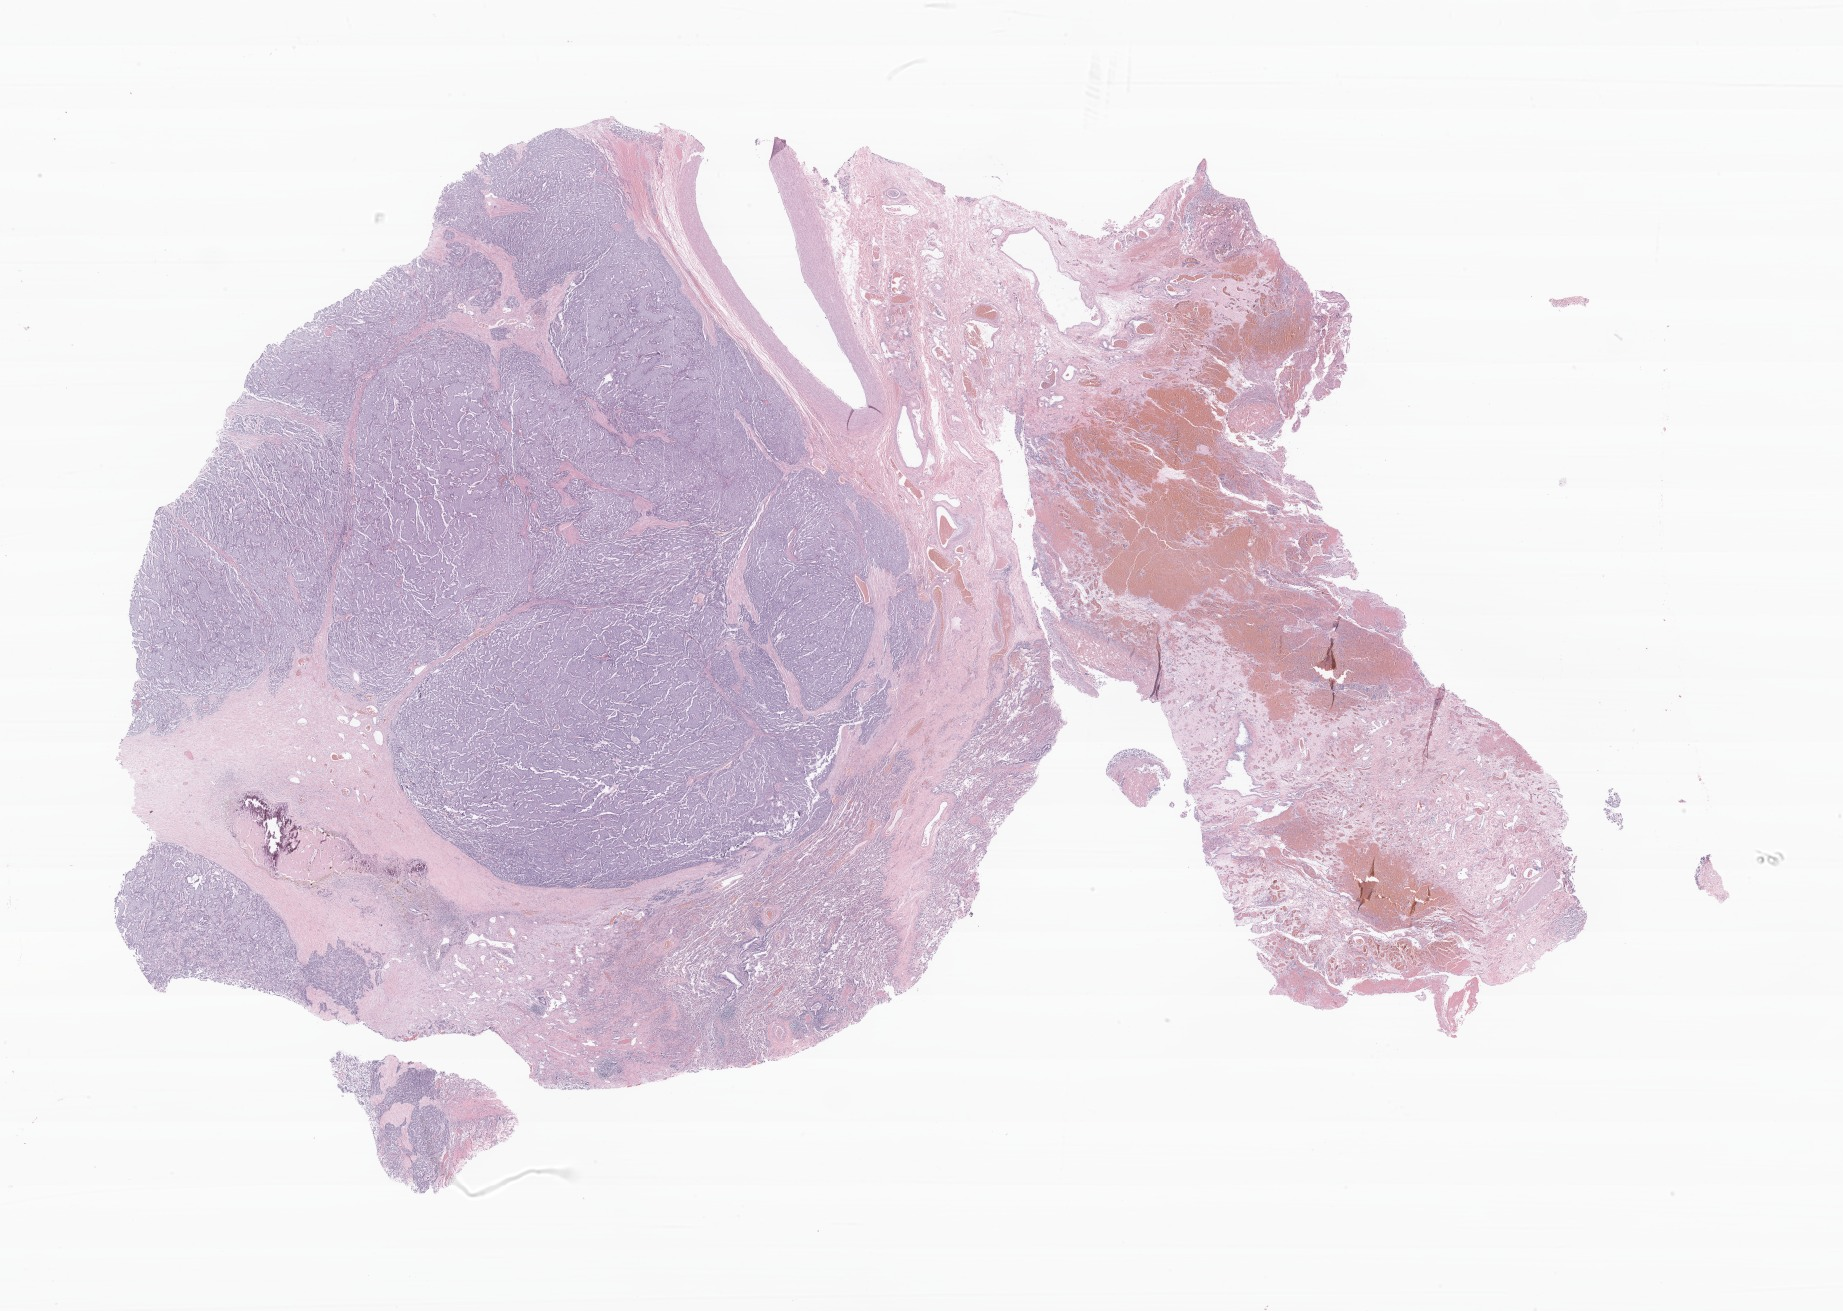
Whole-slide image, haematoxylin and eosin stain of tumor tissue from the lower lobe of lung, shown as a low-resolution overview of the whole scanned area (about 31.0 x 22.1 mm); formalin-fixed, paraffin-embedded (FFPE) tissue. Patient male; age 180 months (15 years).
Diagnosis: Neuroendocrine carcinoma, NOS.